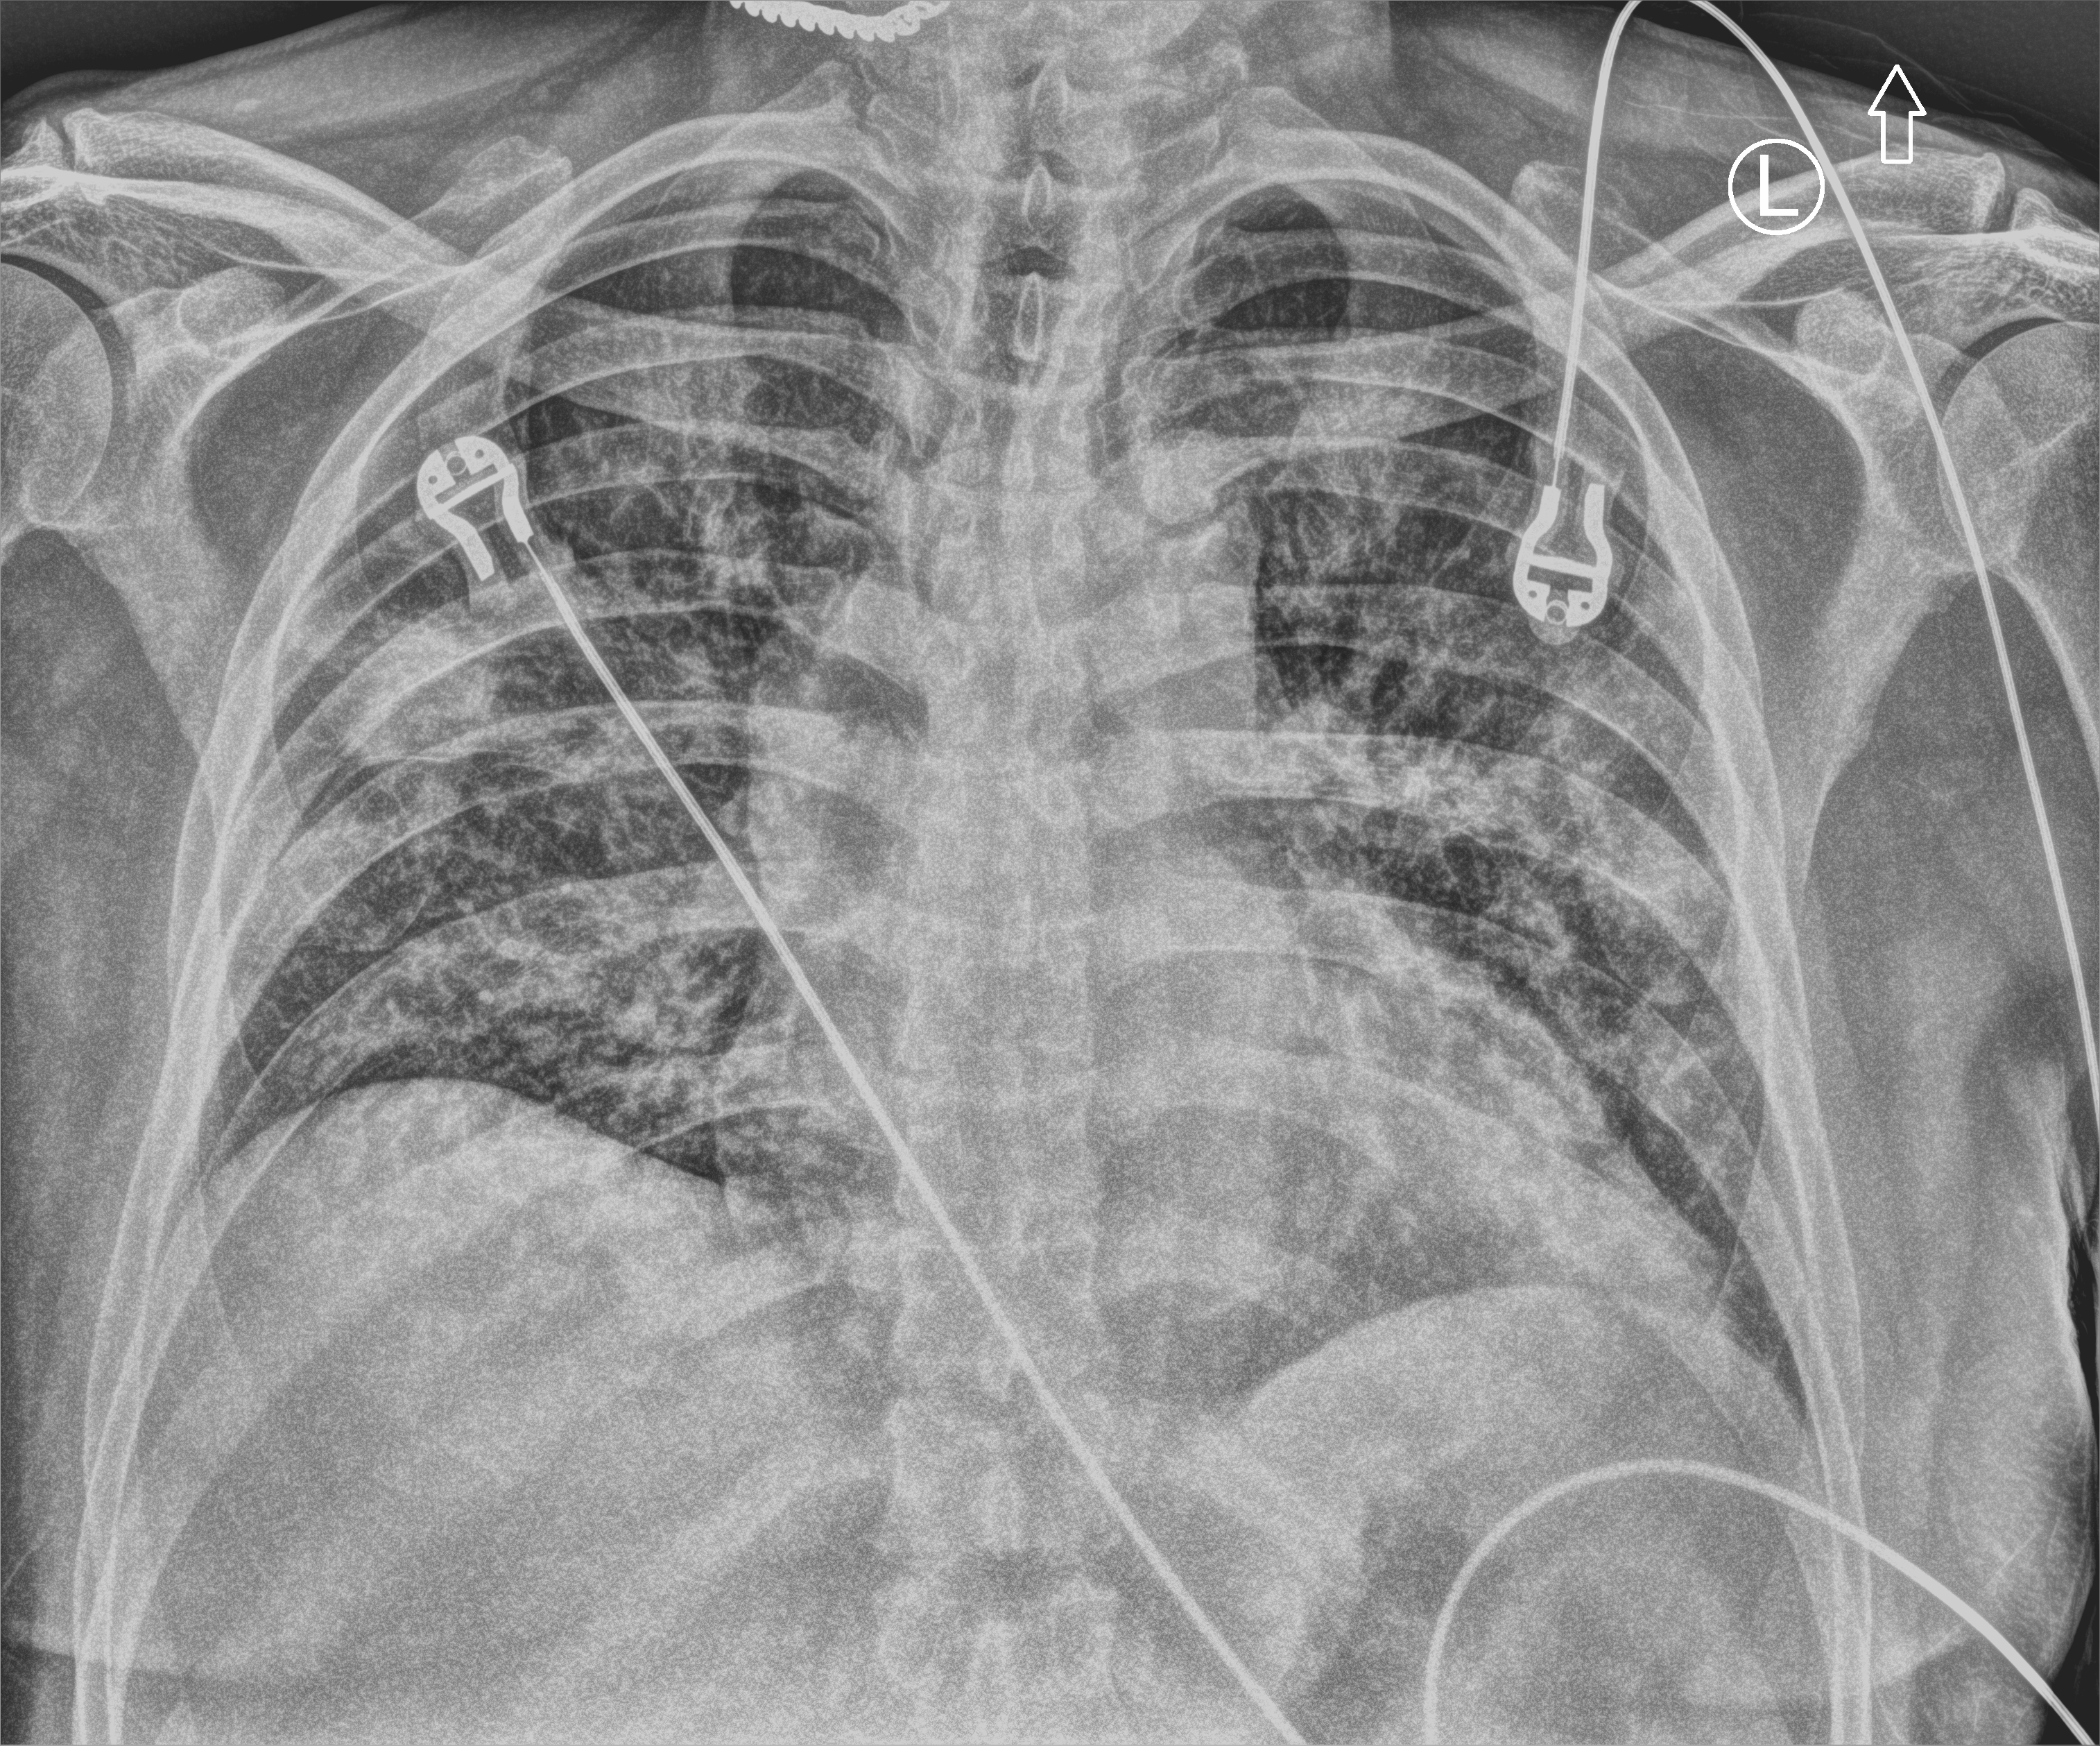
Portable chest radiograph, anteroposterior (AP) projection. Patient hospitalised with COVID-19; male, aged 60–74 years.
Admission-level facts for this patient (not findings on this image; timing relative to this image not recorded): COPD (admission record): no; mechanically ventilated during this hospital stay: no; length of hospital stay: 6 days.